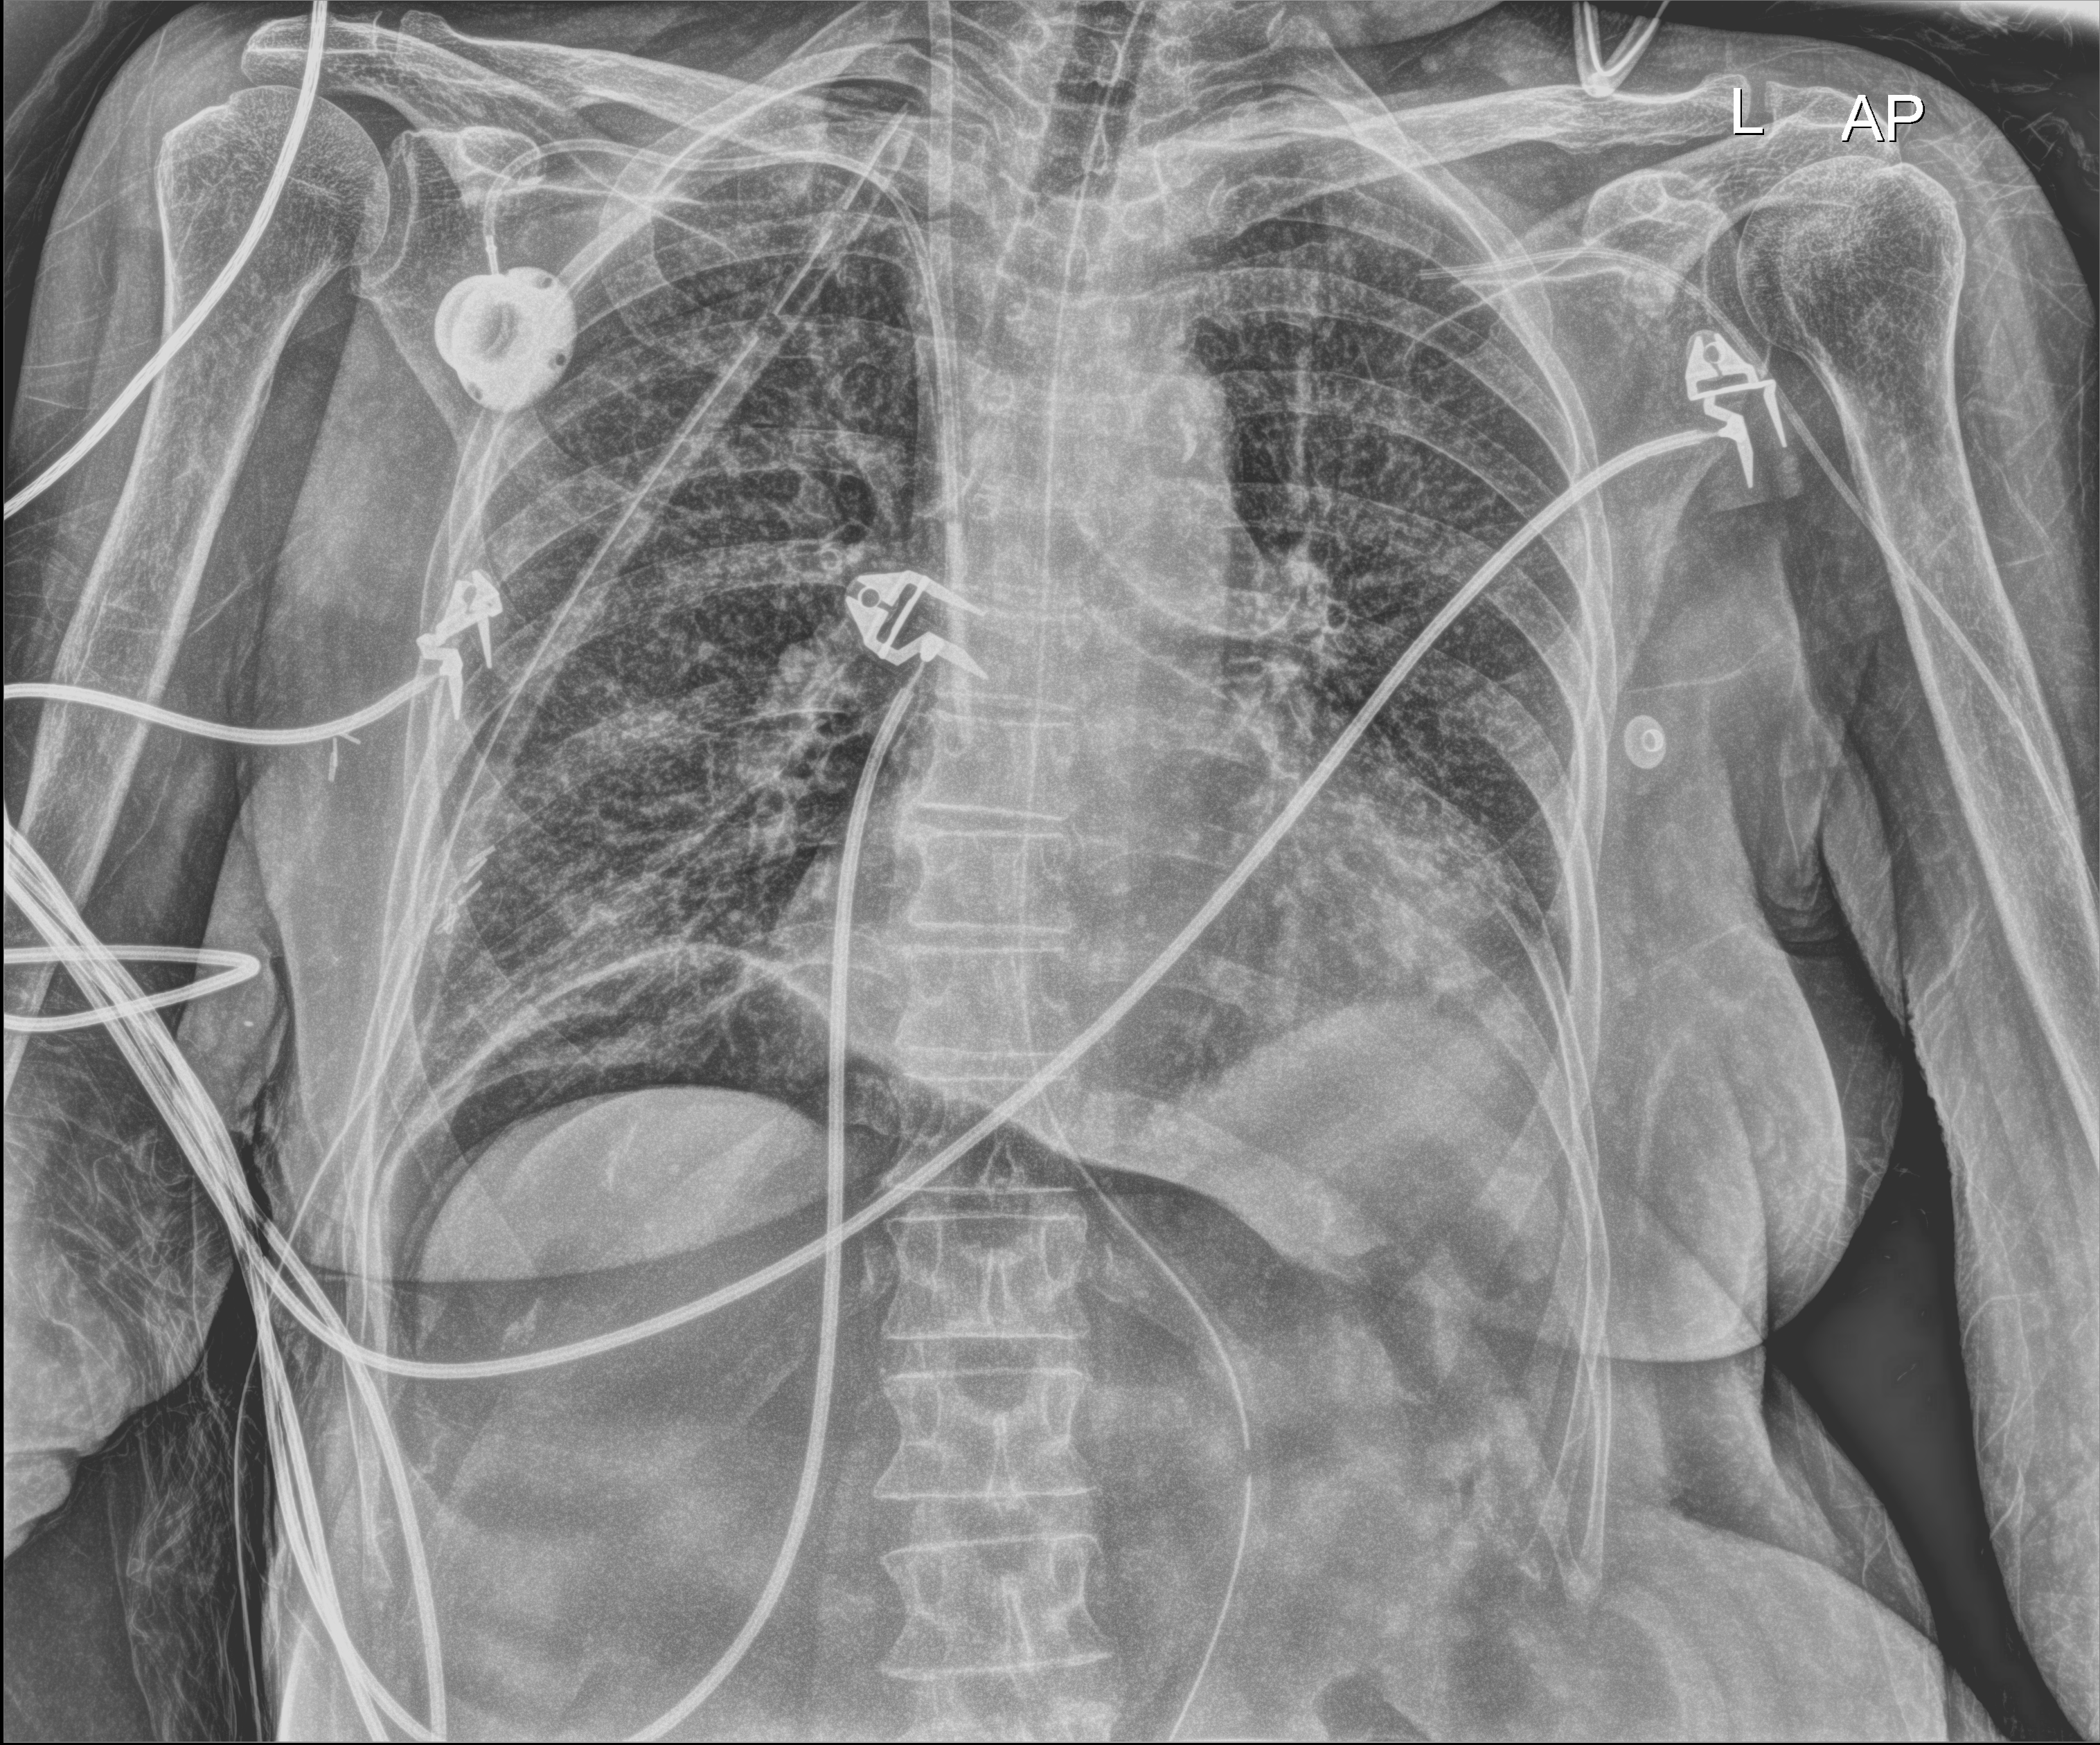
Bedside chest radiograph (digital radiography); anteroposterior (AP) projection. Patient hospitalised with COVID-19; female, aged 60–74 years.
From the hospital-stay record, not from the radiograph (when in the stay this image was taken is not recorded): mechanically ventilated during this hospital stay: yes.